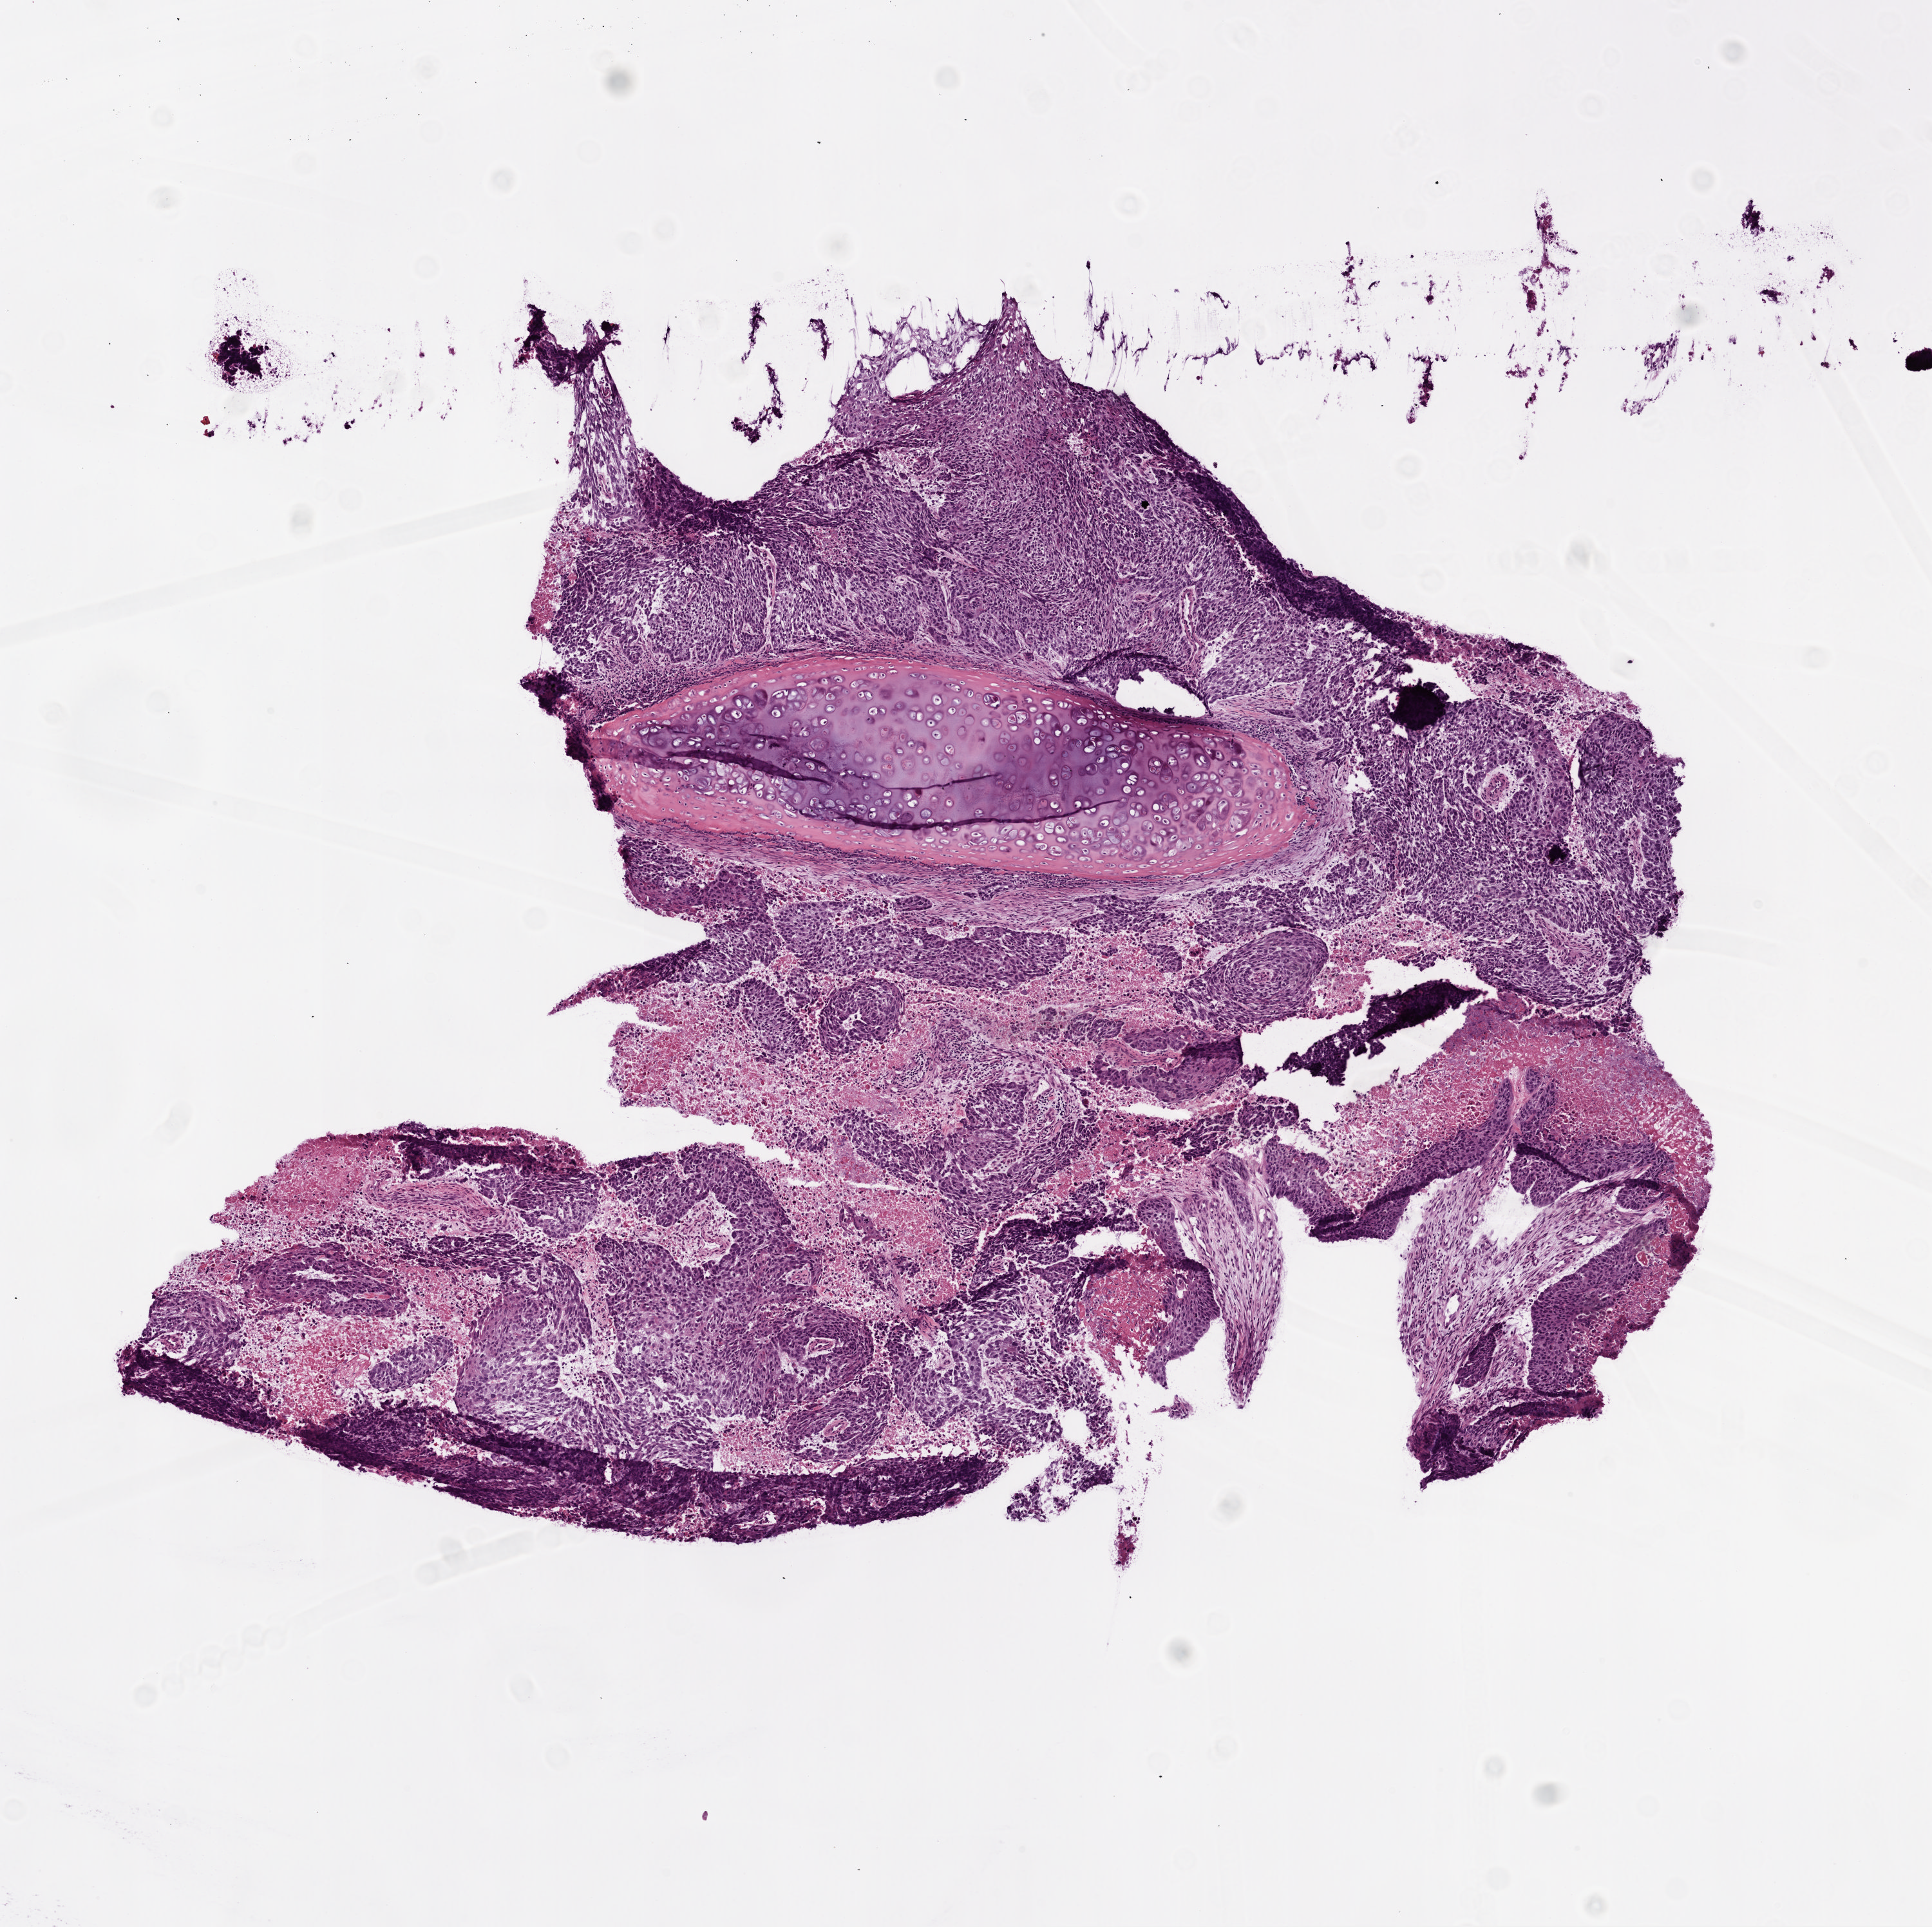
Digitized H&E-stained tissue section (whole slide) — shown as a low-resolution overview of the whole scanned area (about 6.0 x 6.0 mm, slide scanned at 20x), frozen section from the top of the tissue portion, sample: primary tumour, lung. Male, age 66 years at initial diagnosis. Slide review estimates, as recorded: tumour cells 75%, tumour nuclei 85%, normal cells 10%, stromal cells 5%, necrosis 10%.
* AJCC pathologic stage: IIB
* histologic diagnosis: Squamous cell carcinoma, NOS (upper lobe, lung)